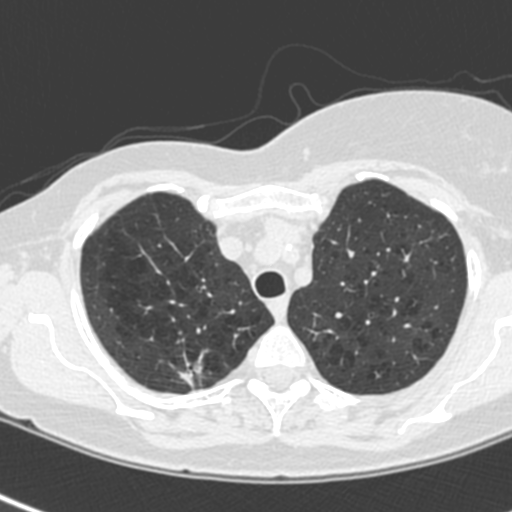
Low-dose screening chest CT, one axial slice. Position 181 of 214 along the scan axis. 120 kVp. Lung window (W 1500 / L -600 HU). 1.3 mm slice thickness. 512 × 512 image matrix, field of view 281 × 281 mm.
Structures marked on this image (manually delineated by an expert):
- lesion 1 (tumor, upper lobe of right lung): bounding box [x1, y1, x2, y2] px = [180, 362, 202, 386]